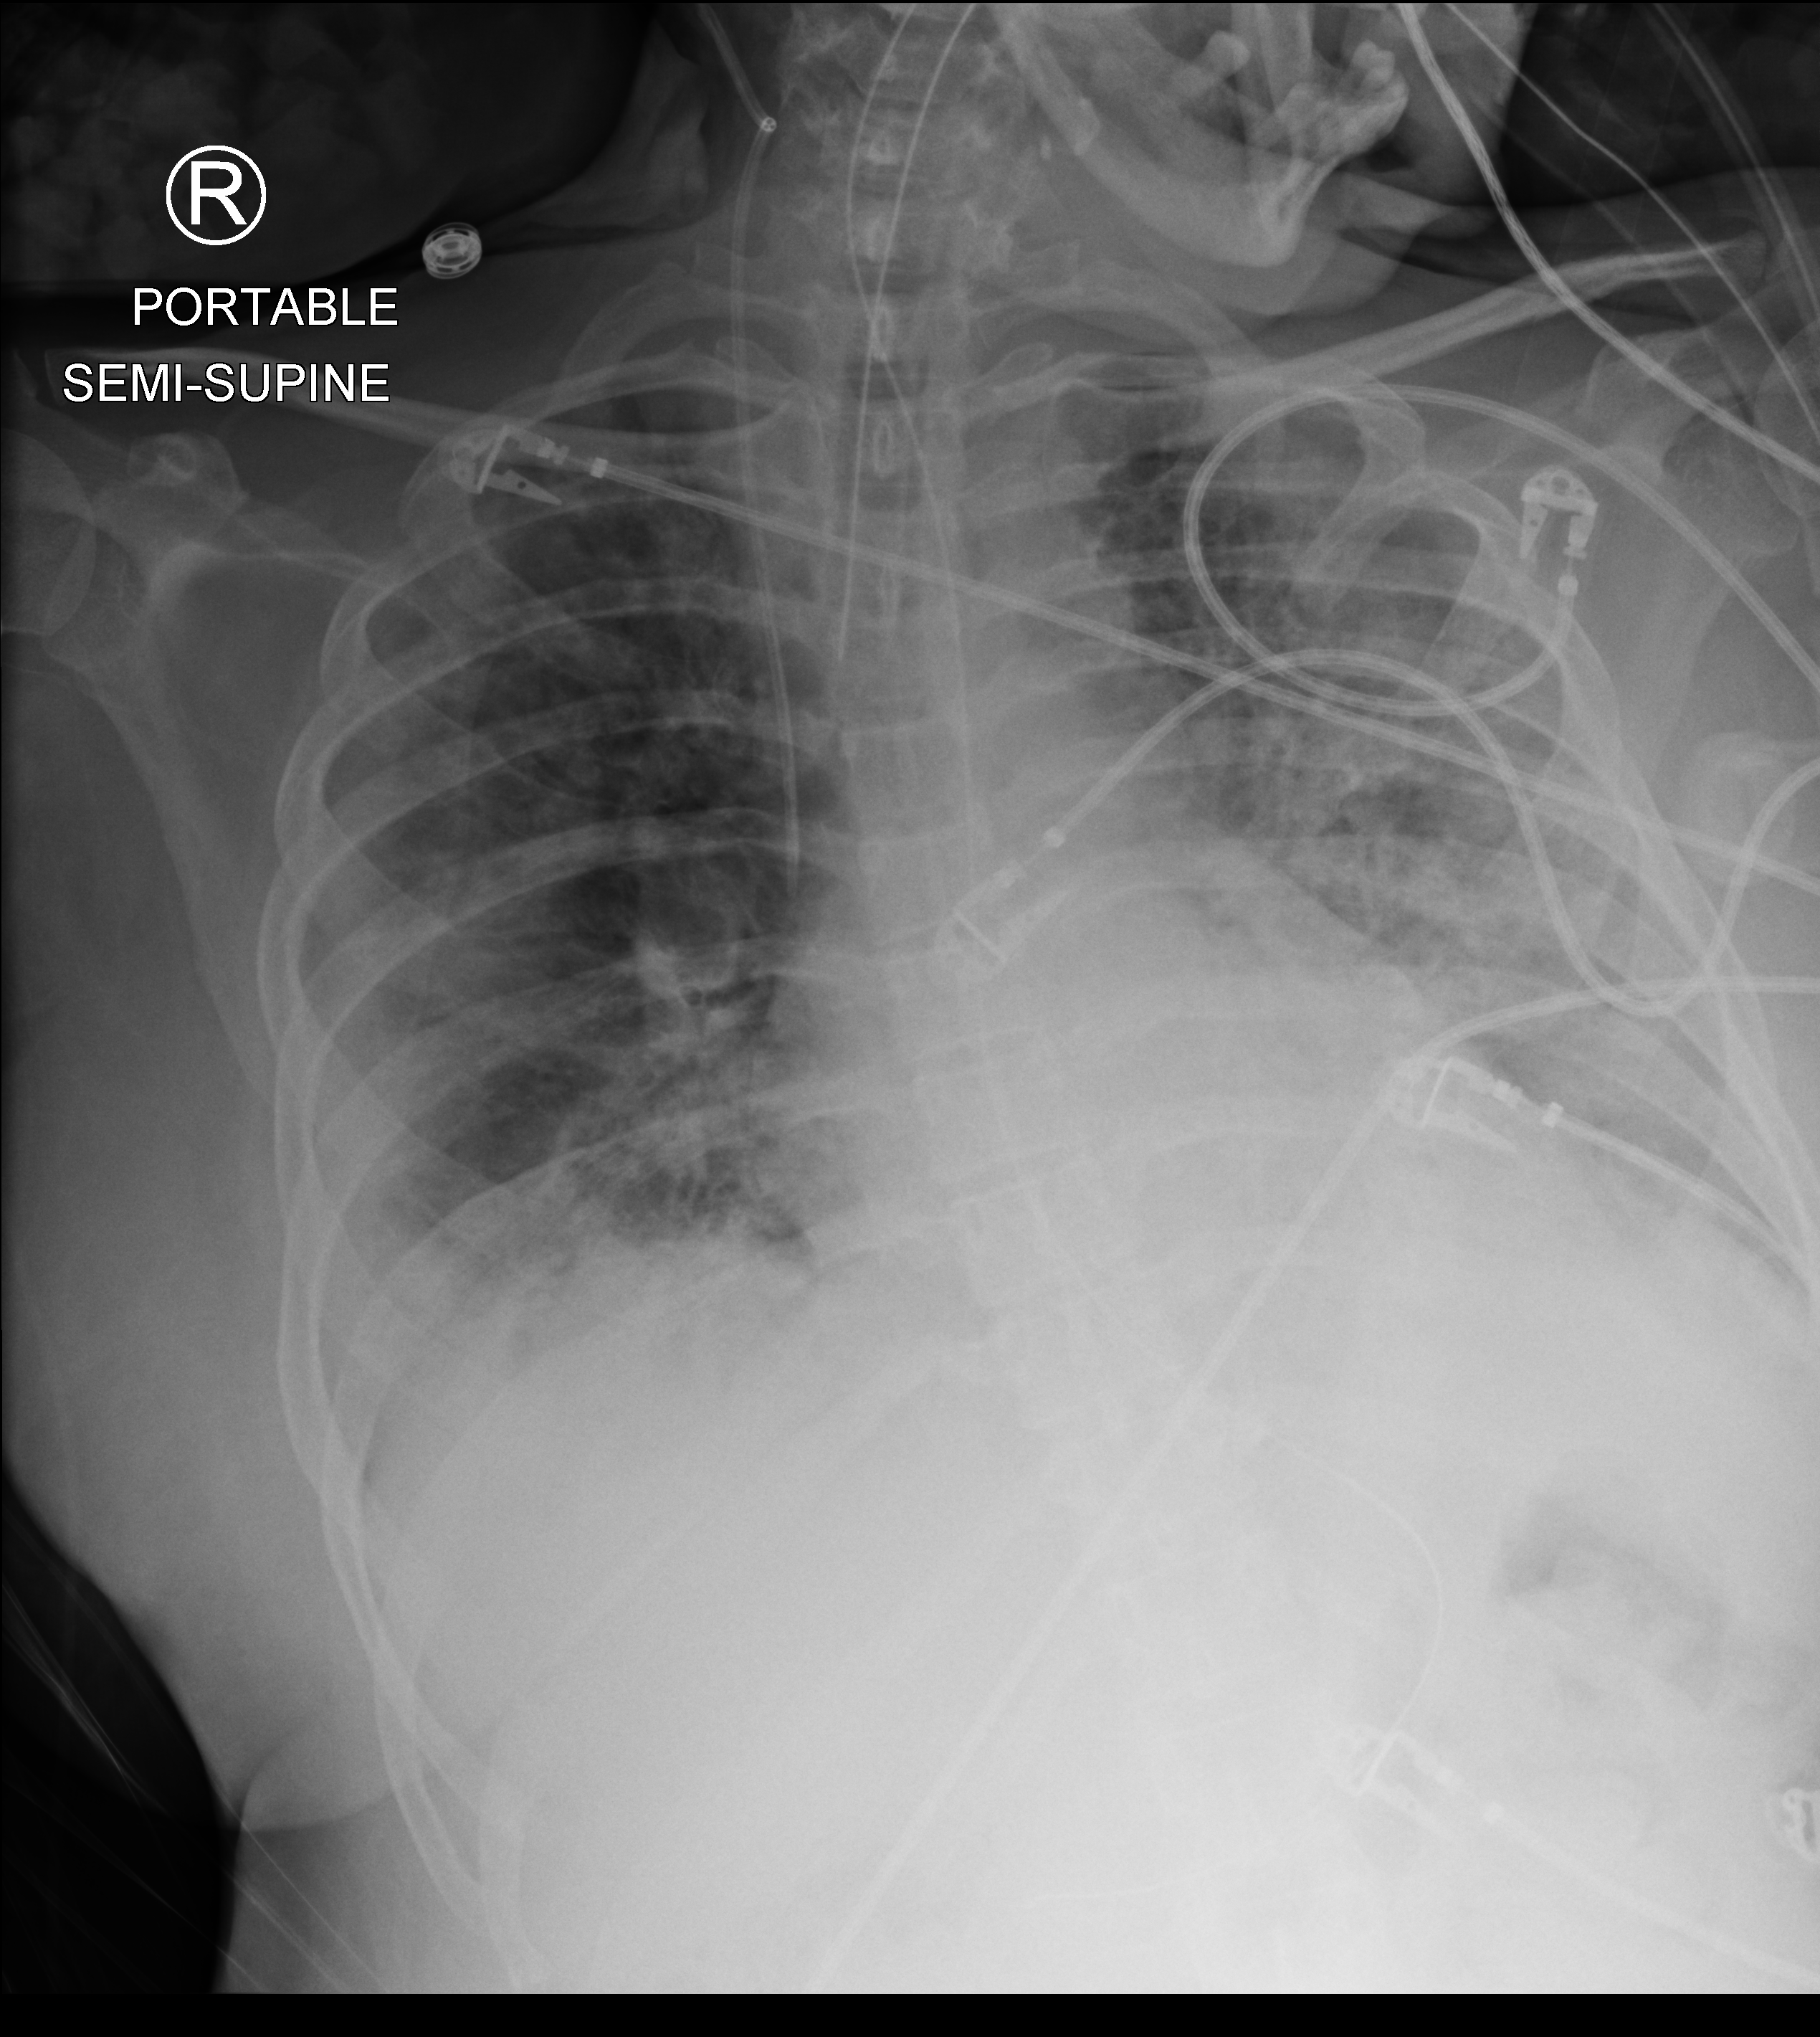
Bedside chest radiograph (computed radiography); anteroposterior (AP) projection. Adult patient hospitalised with COVID-19, age 18–59 years.
Admission-level facts for this patient (not findings on this image; timing relative to this image not recorded):
- admitted to intensive care during this hospital stay: yes
- mechanically ventilated during this hospital stay: yes